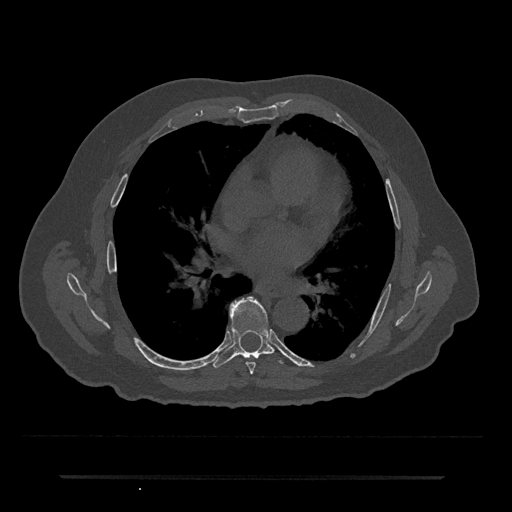
CT including the spine, one axial slice; position 404 of 797 along the scan axis; reconstruction kernel Br40s/3; bone window (W 1800 / L 400 HU); 512 × 512 image matrix. Male patient, age 69 years. From the clinical record (not read from this slice): primary cancer: prostate.
Outlined on this slice (semi-automatically segmented with operator editing):
- T6 vertebra: bounding box [x1, y1, x2, y2] px = [246, 362, 256, 375]
- T7 vertebra: [213, 297, 283, 368]